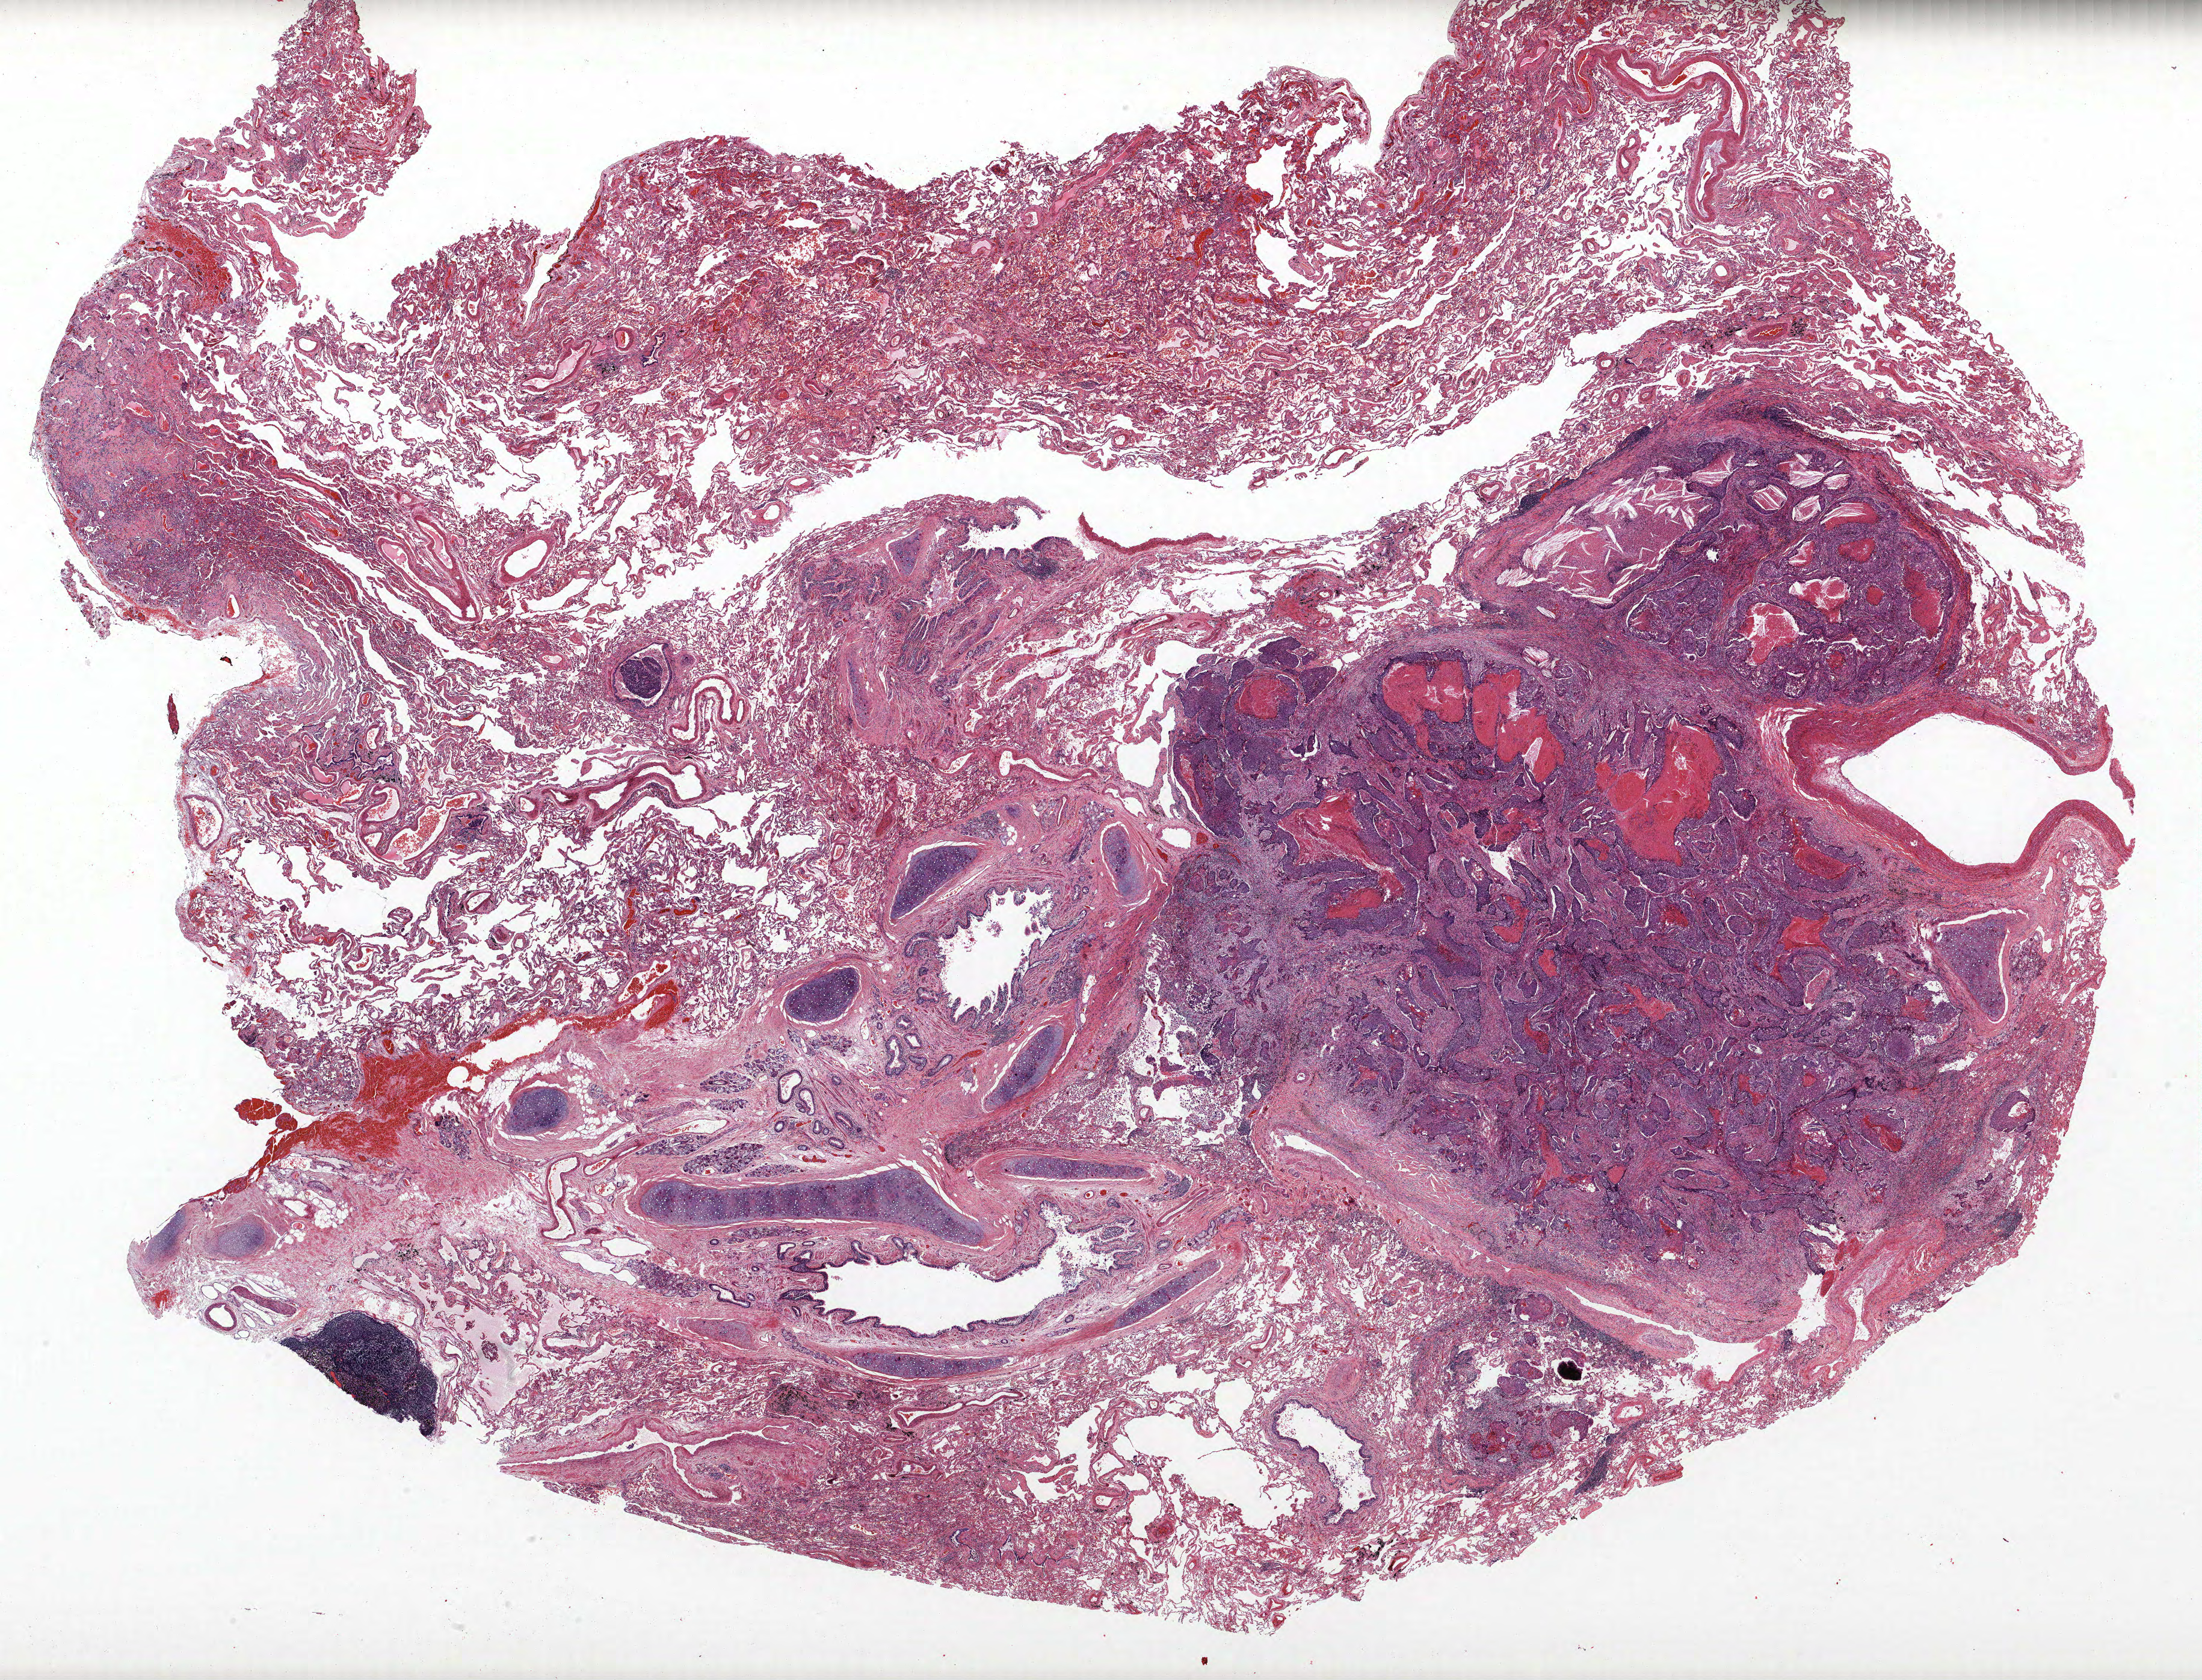
Whole-slide histology image, H&E — low-resolution overview of the scanned area, about 29.3 x 22.3 mm (slide scanned at 40x). Formalin-fixed paraffin-embedded (FFPE) section. Lung tissue. Female, age 65 at enrolment. Former smoker at enrolment. Grade: poorly differentiated (G3).
• primary tumour location (clinical record): right upper lobe
• tumour size (pathology): 35 mm
• participant's lung-cancer diagnosis: Squamous cell carcinoma, NOS (ICD-O-3 8070/3)
• stage (AJCC 6th edition): IB
• ICD-O-3 topography: upper lobe of lung (C34.1)